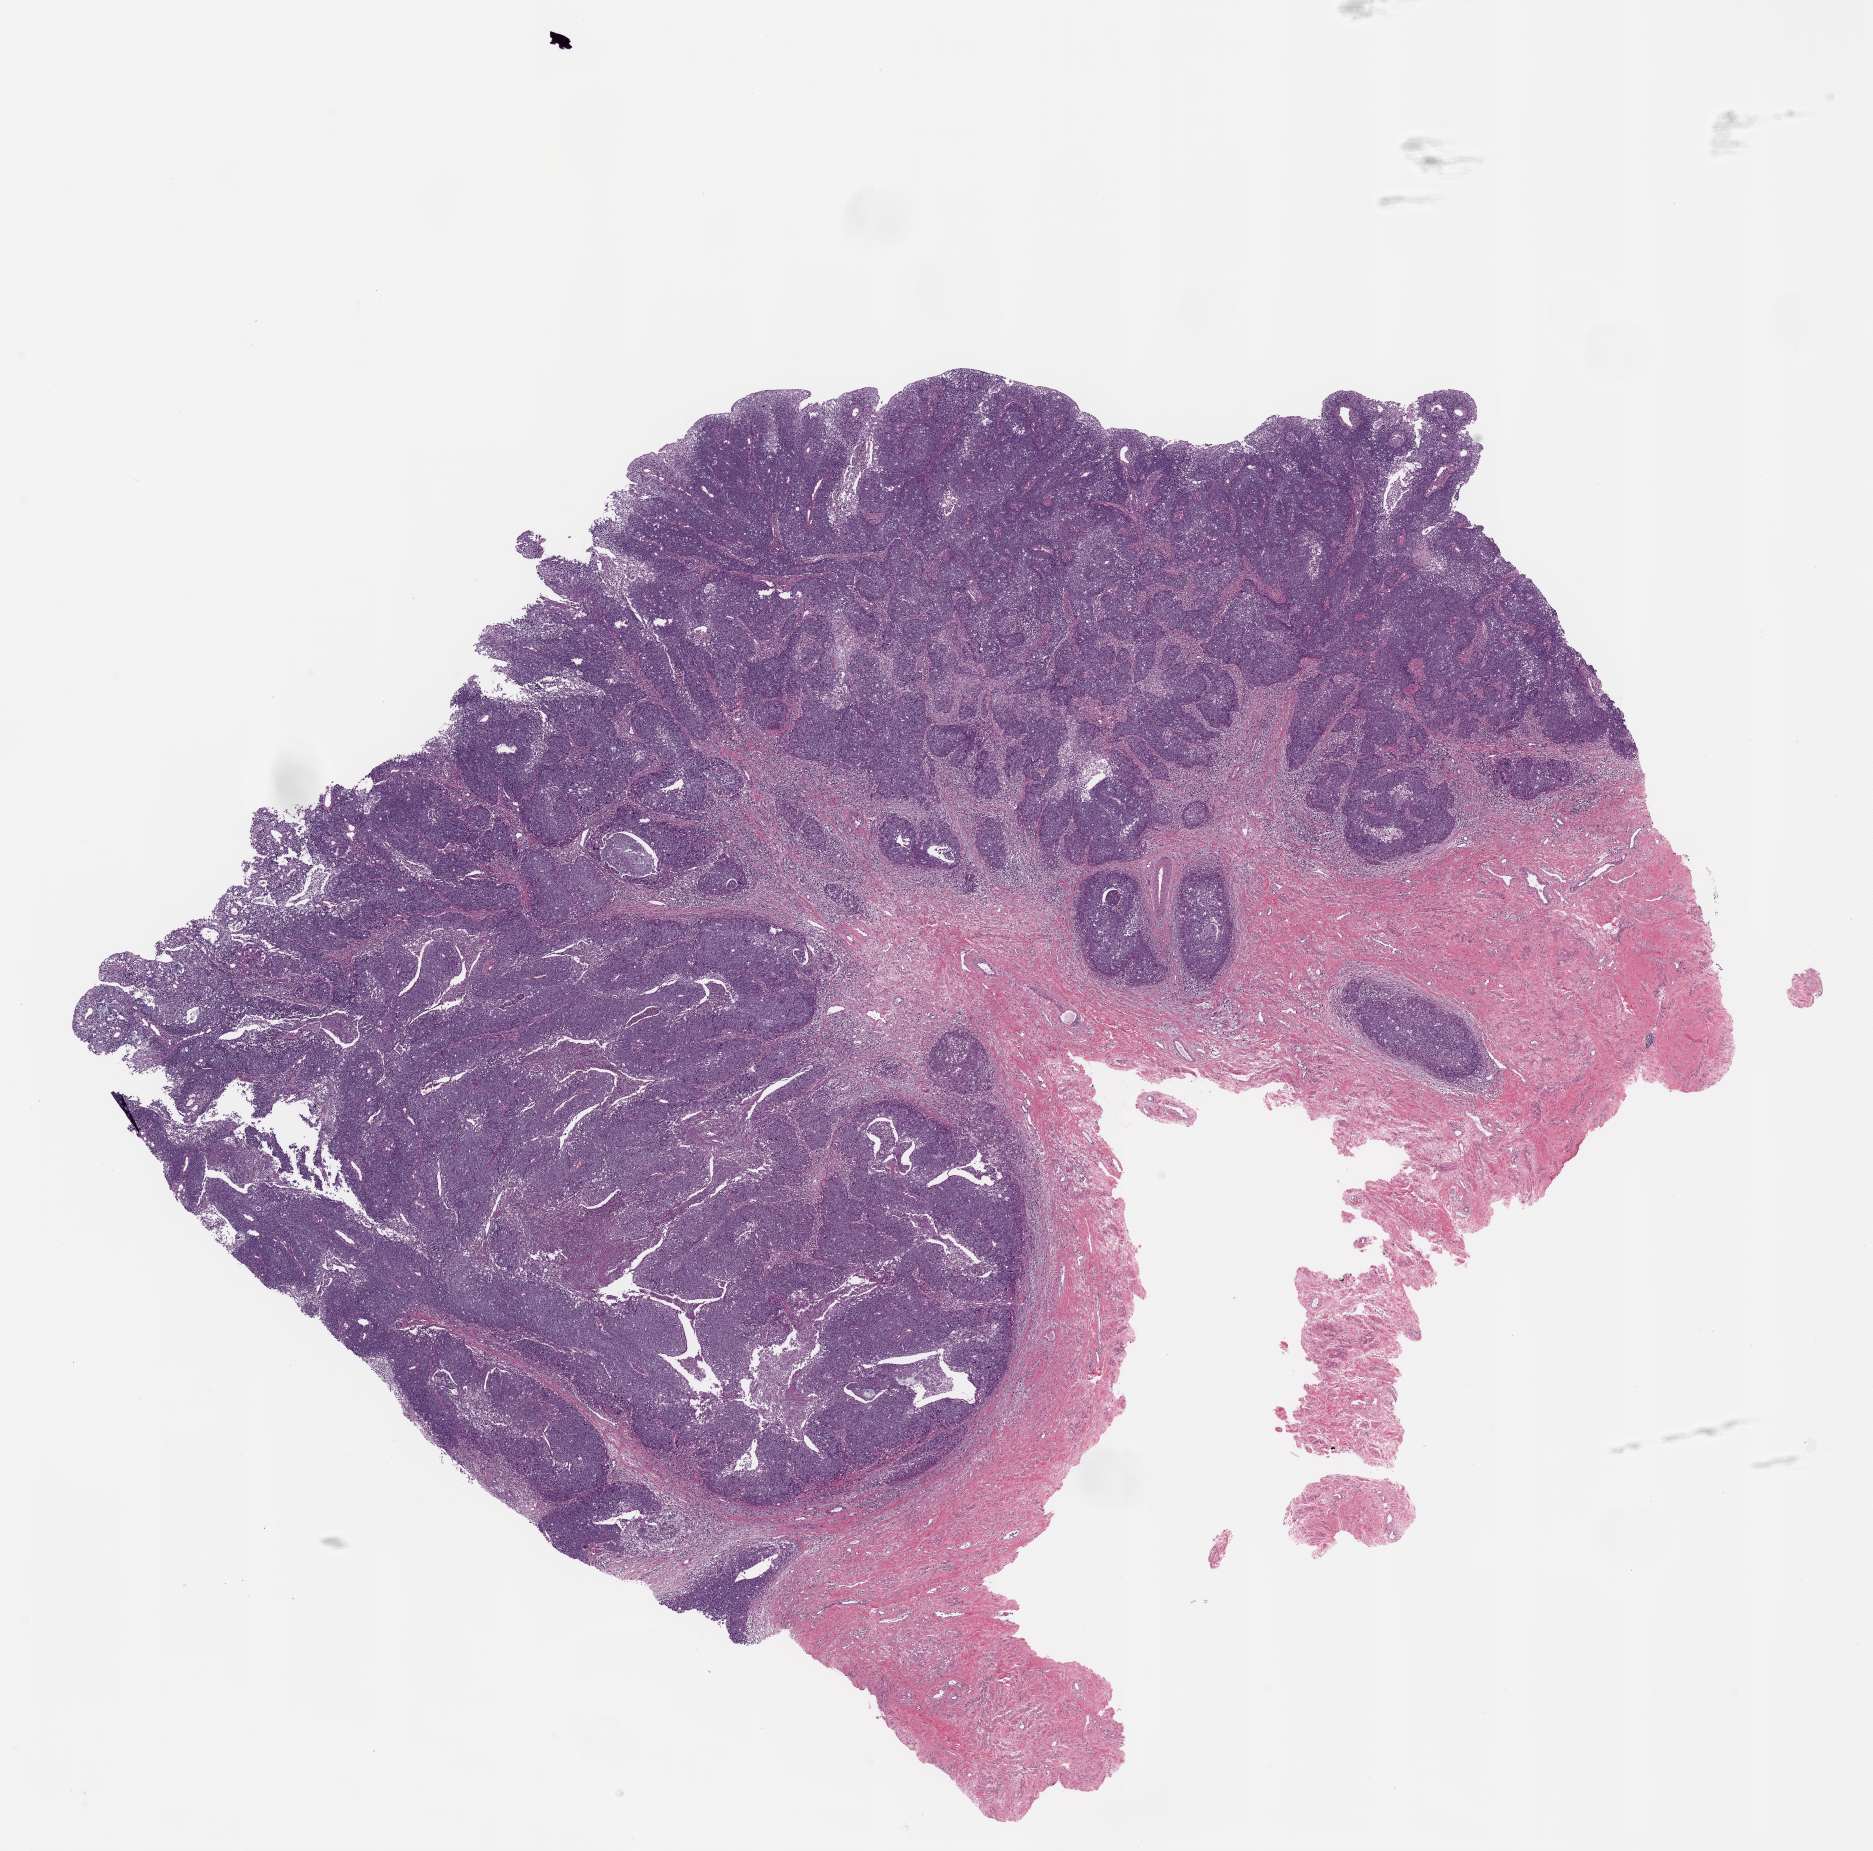
Digitized H&E-stained tissue section (whole slide) — whole scanned area (about 15.0 x 14.8 mm, acquisition: 20x scan) shown as a low-resolution overview, formalin-fixed paraffin-embedded (FFPE) diagnostic section, sample: primary tumour, cervix. Female patient; age at initial diagnosis 51 years. Histologic grade: G3 (poorly differentiated).
FIGO stage: IIIB. Lymph nodes positive (case pathology): 2 of 28 examined. Pathologic diagnosis: Adenocarcinoma, NOS (cervix uteri).